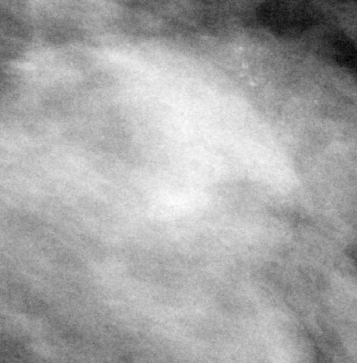
Cropped region of a digitized screen-film mammogram centred on a radiologist-marked abnormality; left breast; MLO view; BI-RADS breast density category 2 (scale 1–4).
Mass, shape round / oval, margins circumscribed / obscured; BI-RADS assessment category 4; pathology (as recorded): benign.